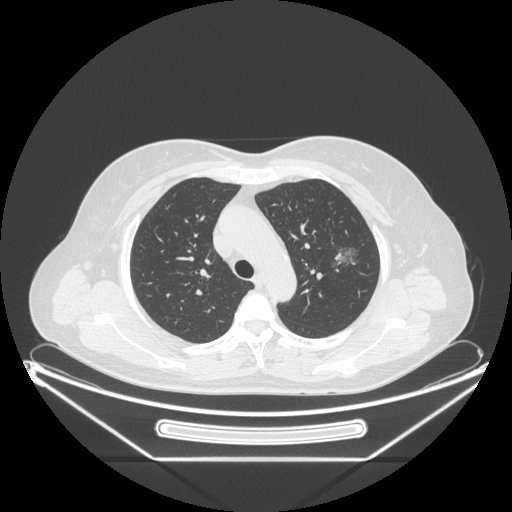
Chest CT, one axial slice; slice 157 of 226 in the series (ordered by position); reconstruction kernel STANDARD; 120 kVp; lung window (W 1500 / L -600 HU); 1.25 mm slice thickness; 512 × 512 image matrix, field of view 447 × 447 mm. Patient: female, 54 years. Case-level facts recorded for this patient, not image findings: clinical TNM (as recorded): T1c N0 M0; histopathological grade: G1.
Annotated regions visible in this slice (bounding box drawn by a radiologist):
- lung tumour (recorded histology: adenocarcinoma): bounding box [x1, y1, x2, y2] px = [325, 242, 371, 285]